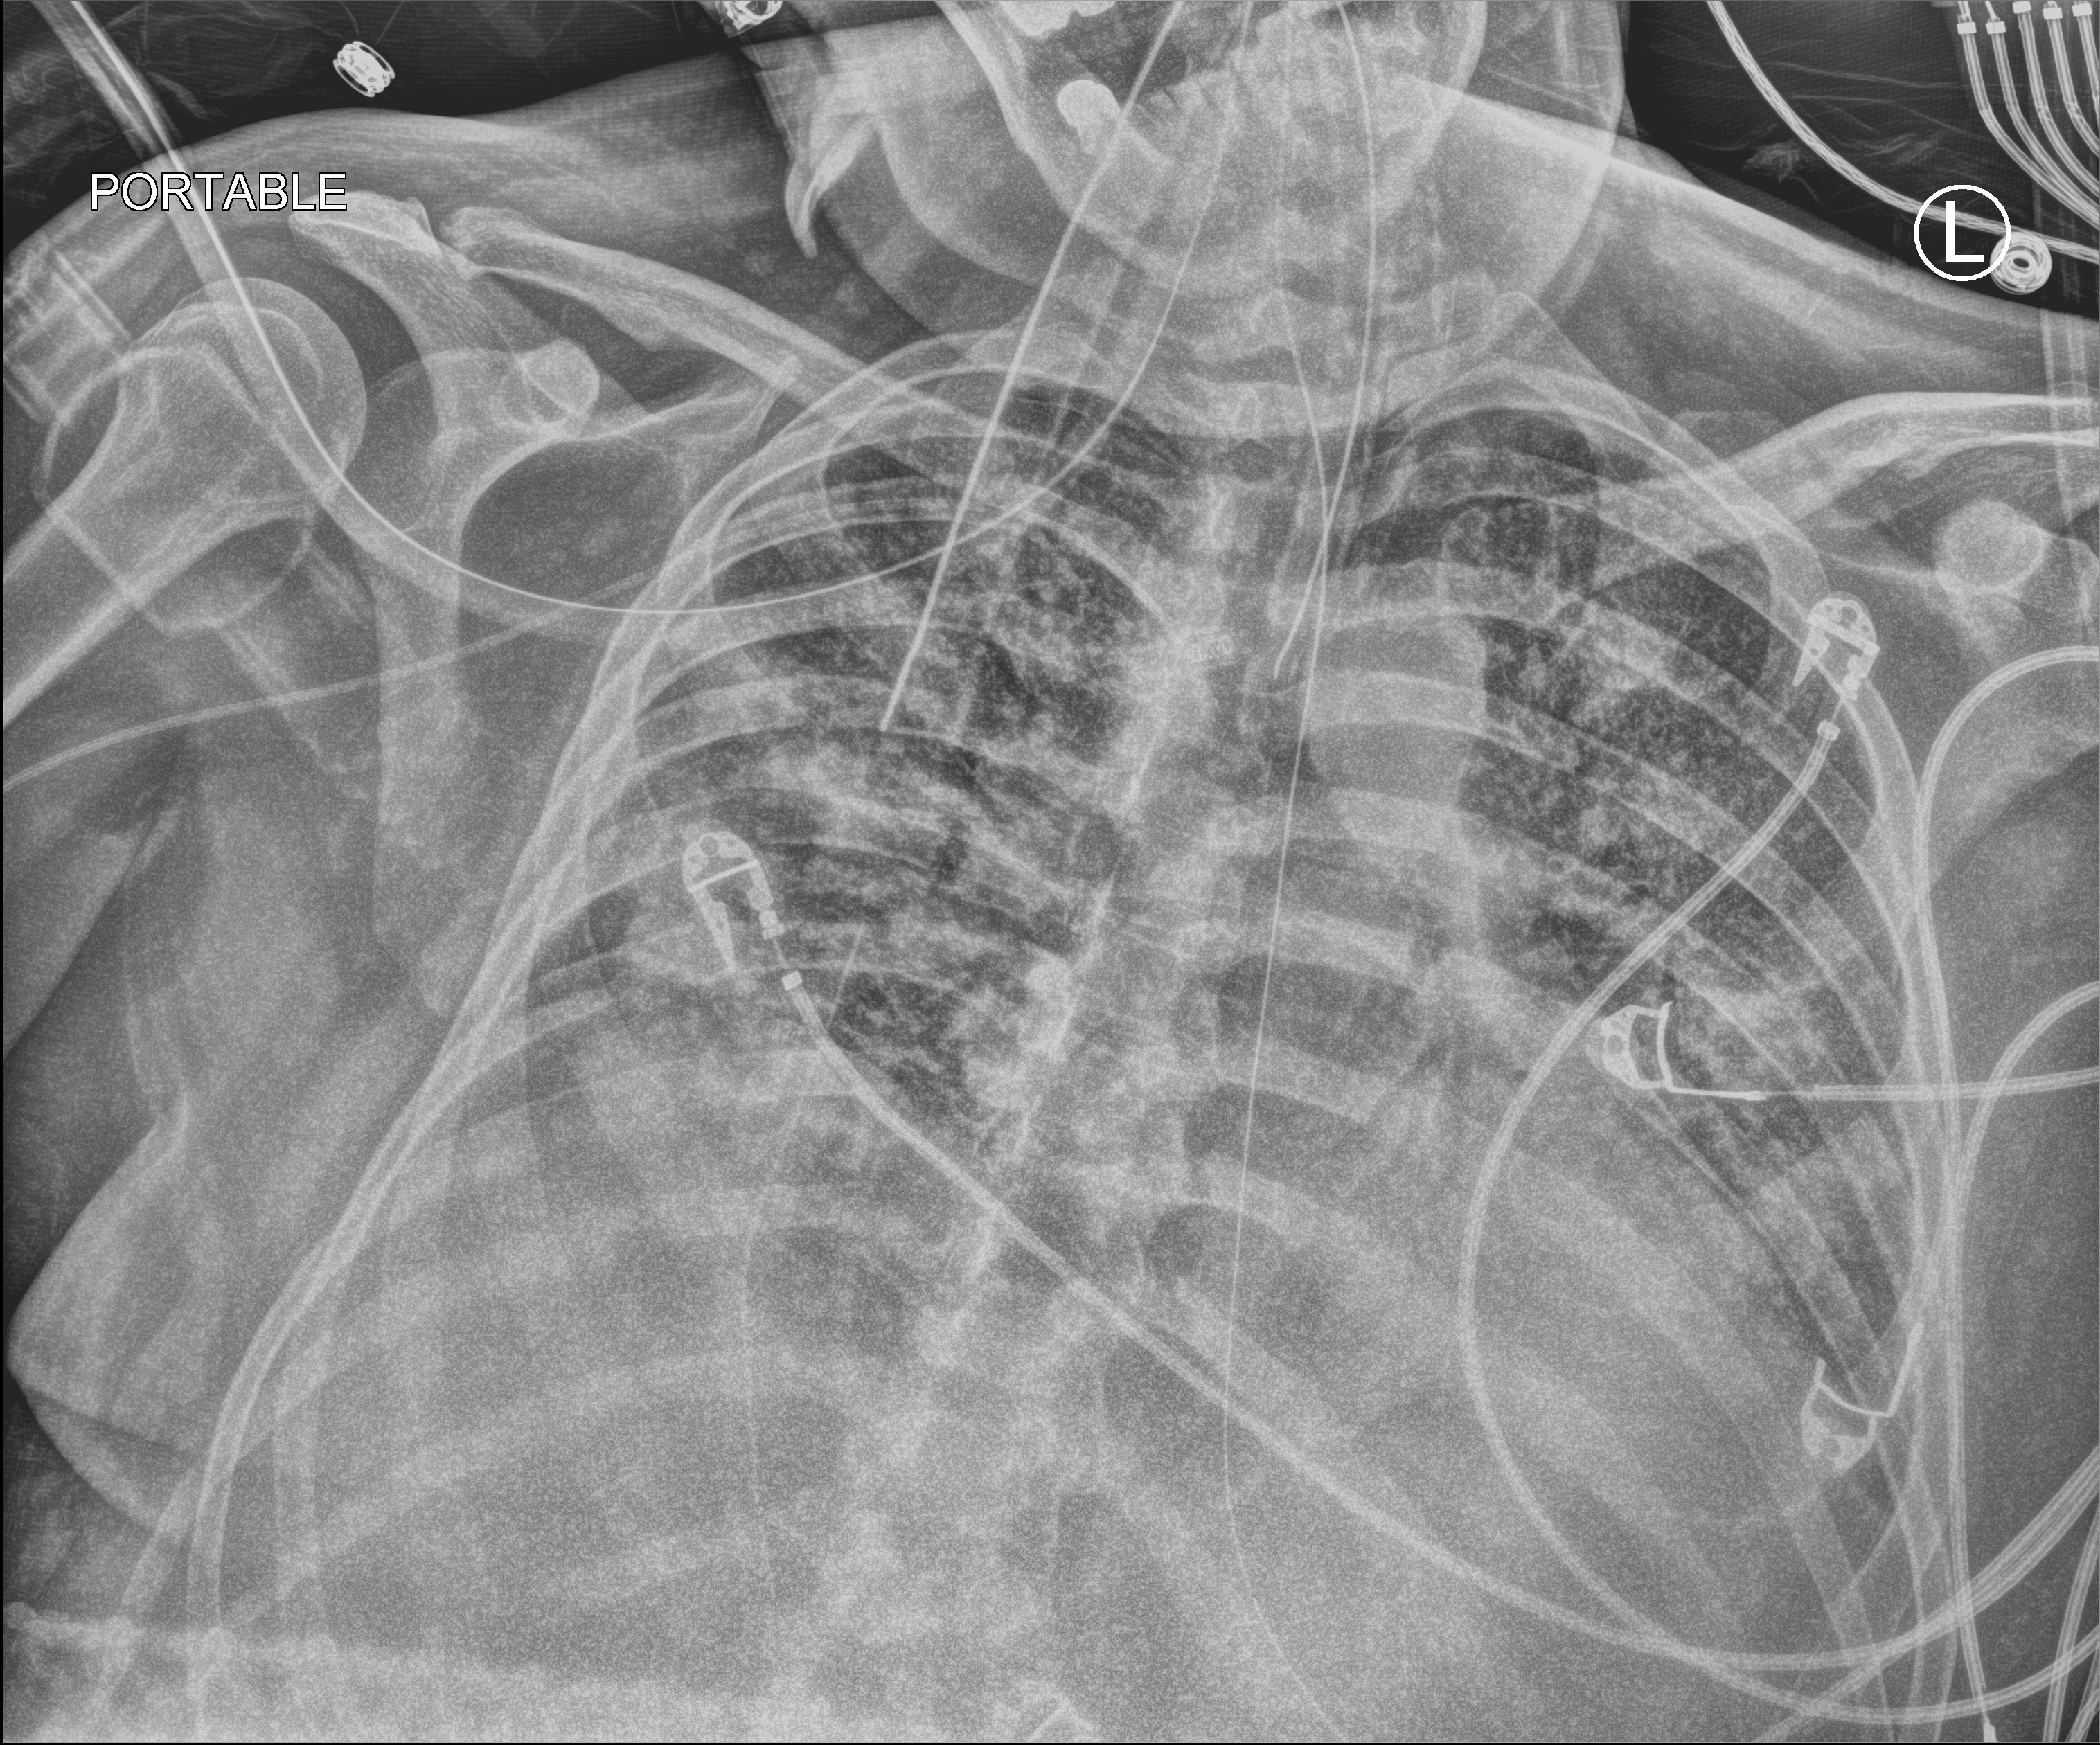
Portable chest radiograph. Male patient hospitalised with COVID-19, age 18–59 years.
Hospital-stay facts (about this admission, not read from this image; timing relative to this image not recorded): admitted to intensive care during this hospital stay: yes; length of hospital stay: 96 days.